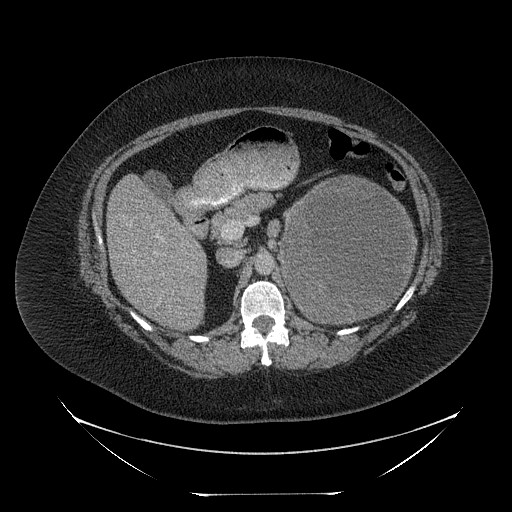
Contrast-enhanced abdominal CT, one axial slice. Slice 139 of 205 in the series (ordered by position). Reconstruction kernel STANDARD. Intravenous contrast given. Soft-tissue window (W 400 / L 40 HU). 2.5 mm slice thickness. 512 × 512 image matrix, field of view 500 × 500 mm. Female patient, age 53 years. From the clinical record (not read from this slice): diagnosis: adrenocortical carcinoma; tumour side: left adrenal; tumour size at pathology: 17 cm; Ki-67 index: 20 %; stage (as recorded): 3.
Annotated regions visible in this slice (semi-automatically segmented with operator editing):
- mass: bounding box [x1, y1, x2, y2] px = [283, 179, 412, 320]